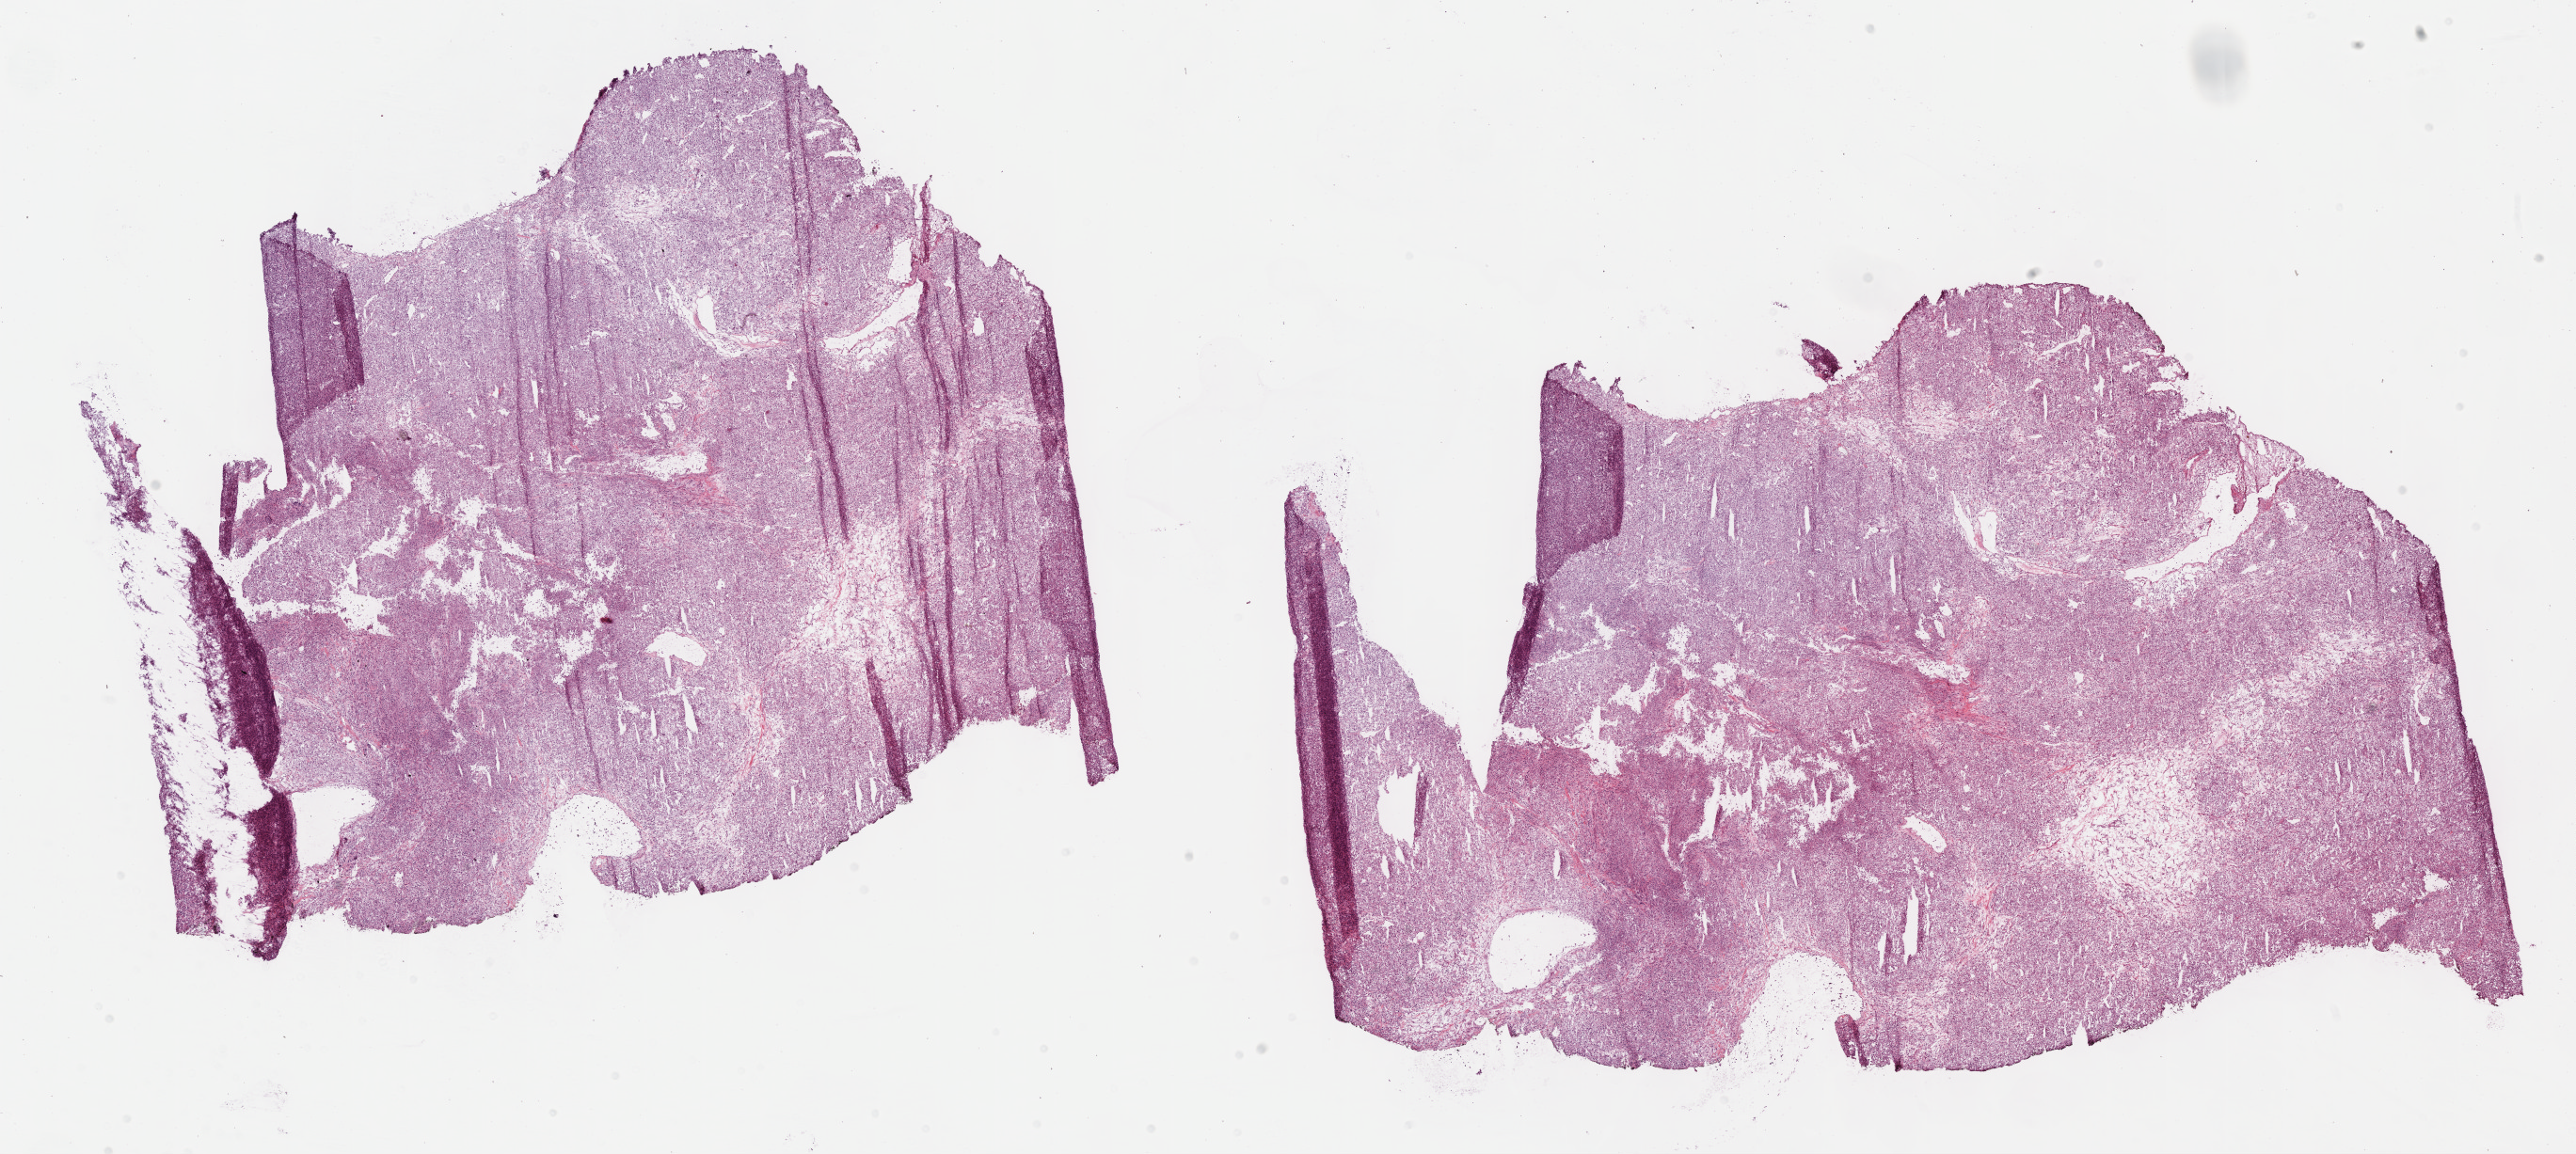
Hematoxylin and eosin (H&E) stained whole-slide image, shown as a low-resolution overview of the whole scanned area (about 22.1 x 9.9 mm, acquisition: 40x scan), frozen section from the bottom of the tissue portion, sample: primary tumour, kidney. Male patient; age at initial diagnosis 46 years. Histologic grade: G3 (poorly differentiated). Pathologist review of this section (percent, as recorded): tumour cells 95%, tumour nuclei 85%, normal cells 0%, stromal cells 5%, necrosis 0%.
• AJCC pathologic stage: IV
• diagnosis: Clear cell adenocarcinoma, NOS